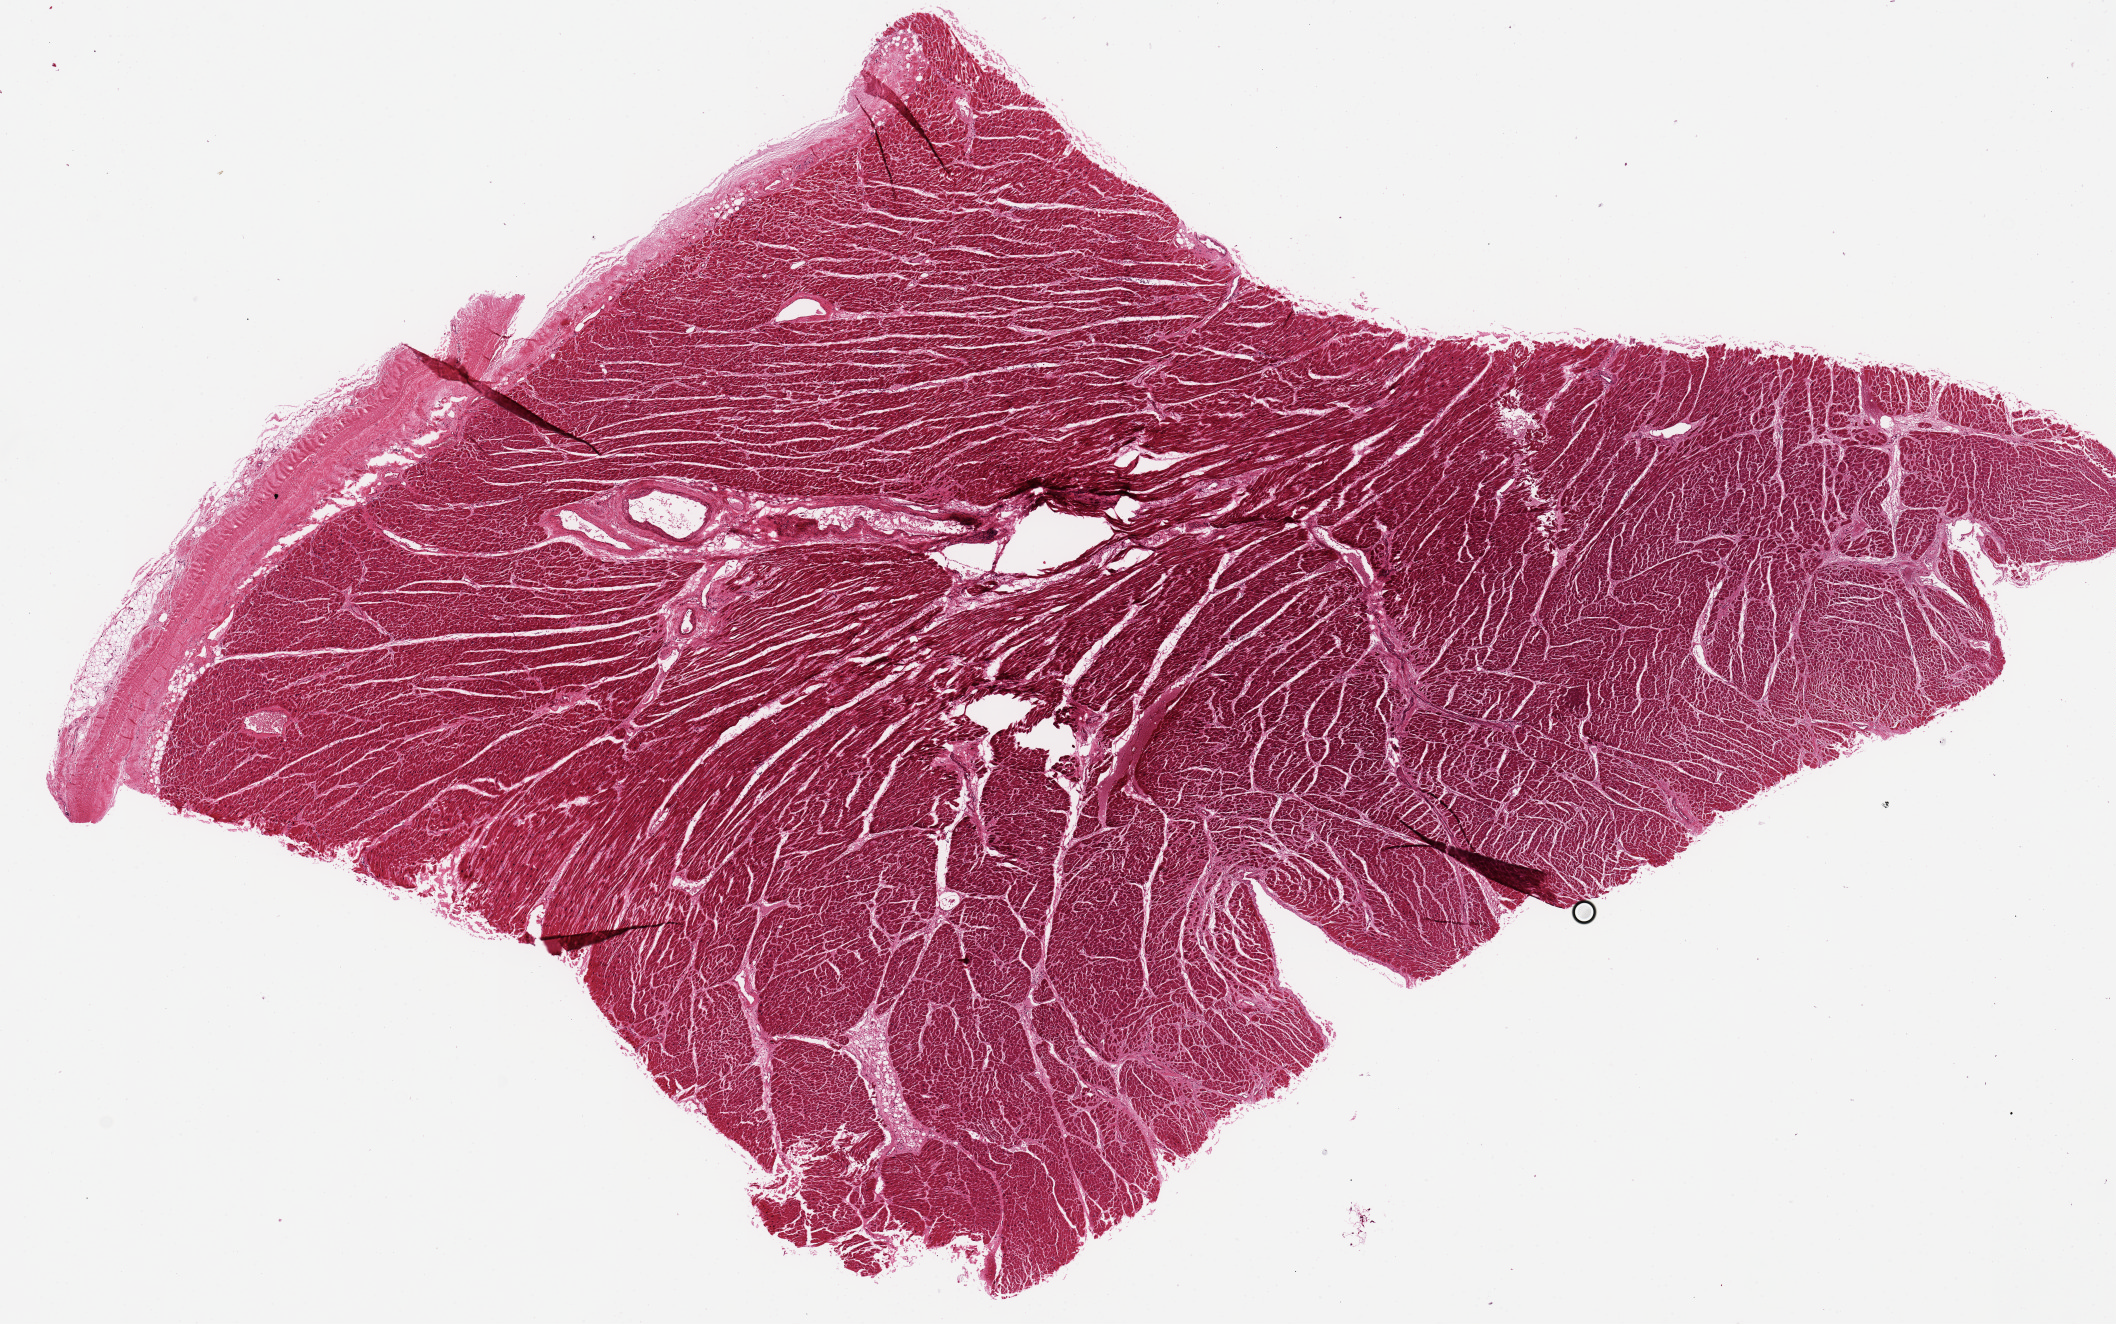
Whole-slide image, hematoxylin and eosin (H&E) stain, brightfield — a low-resolution overview of the entire scanned area, about 16.7 x 10.5 mm (acquisition: 20x scan); PAXgene-fixed paraffin-embedded (PFPE) section; target tissue: heart; donor tissue sample.
- review note (as recorded): Minimal interstitial fibrosis